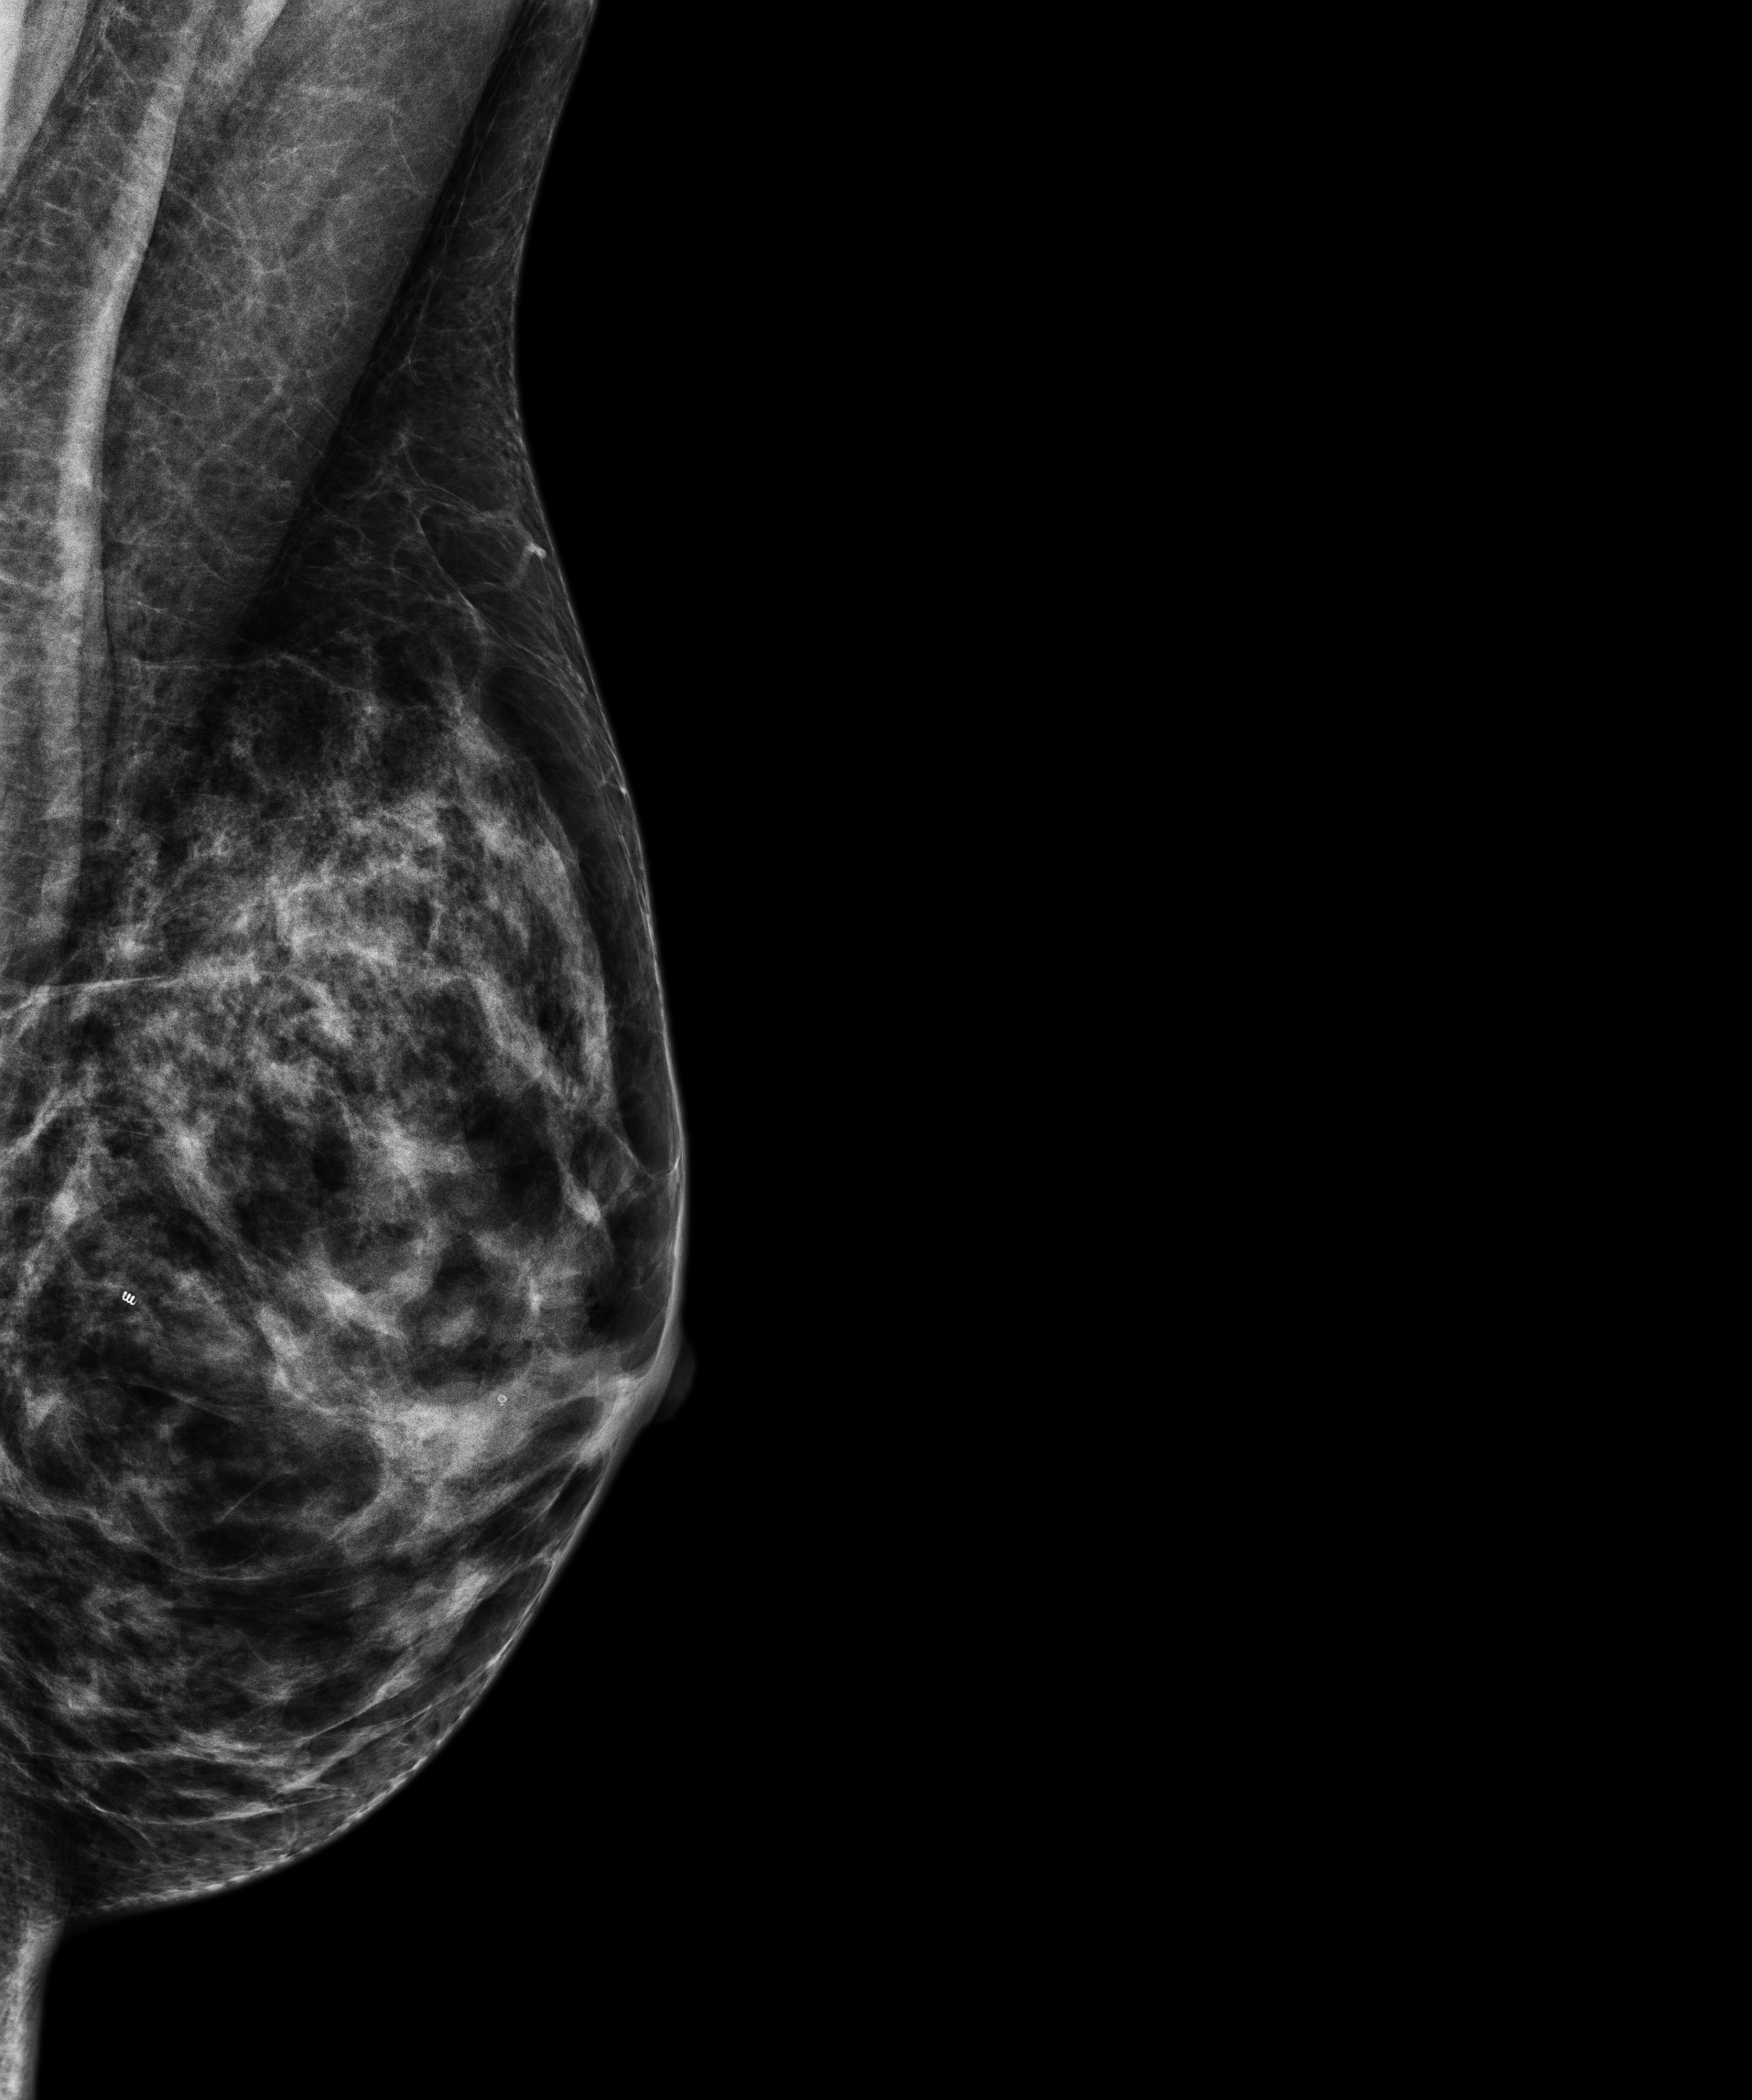
Annual screening mammography examination; compressed breast thickness 51.8 mm. Patient aged 44 years (female).
Image type: full-field digital mammogram. Breast: left. Projection: mediolateral oblique (MLO) view.